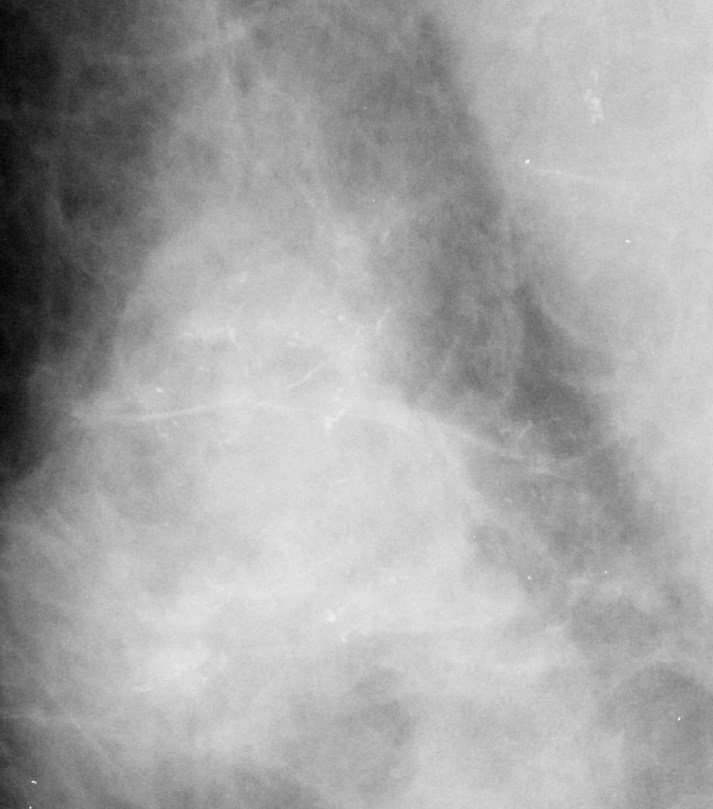
Crop from a digitized film mammogram around one marked abnormality, right breast, MLO view.
- Marked abnormality: calcifications, morphology fine linear branching, distribution segmental; BI-RADS assessment category 5; subtlety rating 3 on a 1 (subtle) to 5 (obvious) scale; pathology (as recorded): malignant.